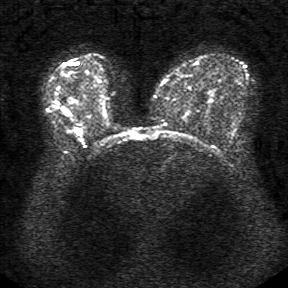
Breast MRI, one axial slice; position 19 of 34 along the scan axis; diffusion-weighted series; image 2 of 4 stored at this slice position (different b-values; order by instance number); 1.5 T; 288 × 288 image matrix. Female patient.
Annotated regions visible in this slice (outlined manually by an expert reader):
- tumour on diffusion-weighted imaging: bounding box [x1, y1, x2, y2] px = [69, 98, 73, 102]